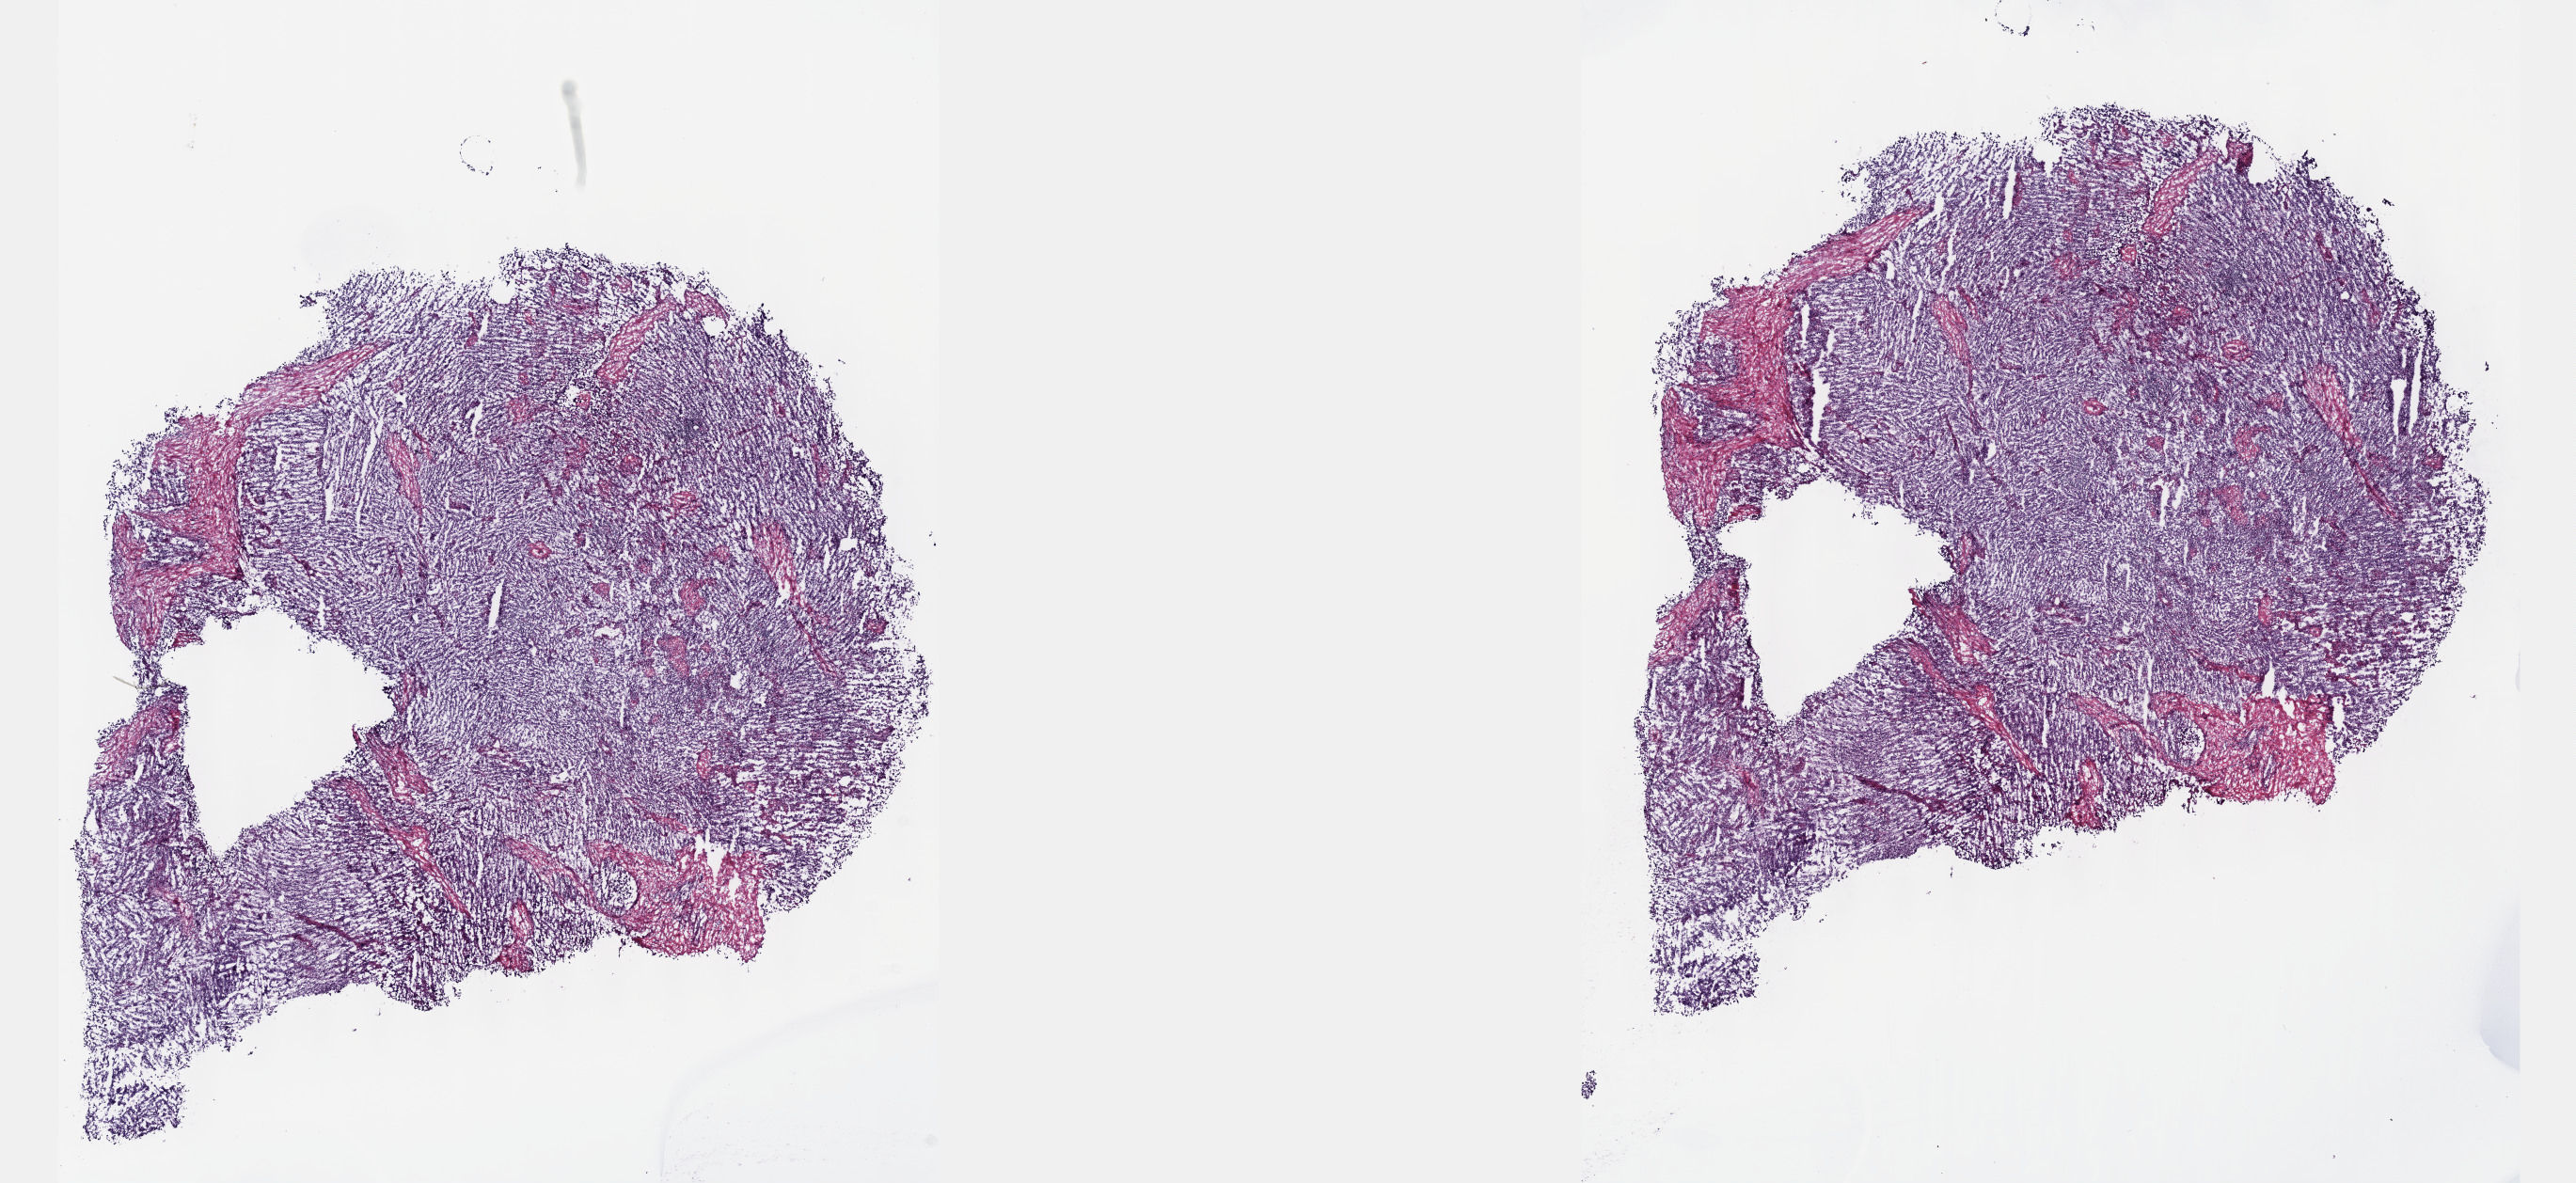
Digitized H&E-stained tissue section (whole slide), low-resolution overview of the scanned area, about 22.1 x 10.2 mm, frozen section from the top of the tissue portion, primary tumour sample from the testis. Male patient; age at initial diagnosis 44 years. Pathologist review of this section (percent, as recorded): tumour cells 100%, tumour nuclei 75%, normal cells 0%, stromal cells 0%, necrosis 0%. Inflammatory infiltration, as recorded: lymphocyte infiltration 1%, monocyte infiltration 0%, neutrophil infiltration 0%.
* pathologic diagnosis: Seminoma, NOS
* AJCC pathologic stage: IB (7th edition)
* laterality: right